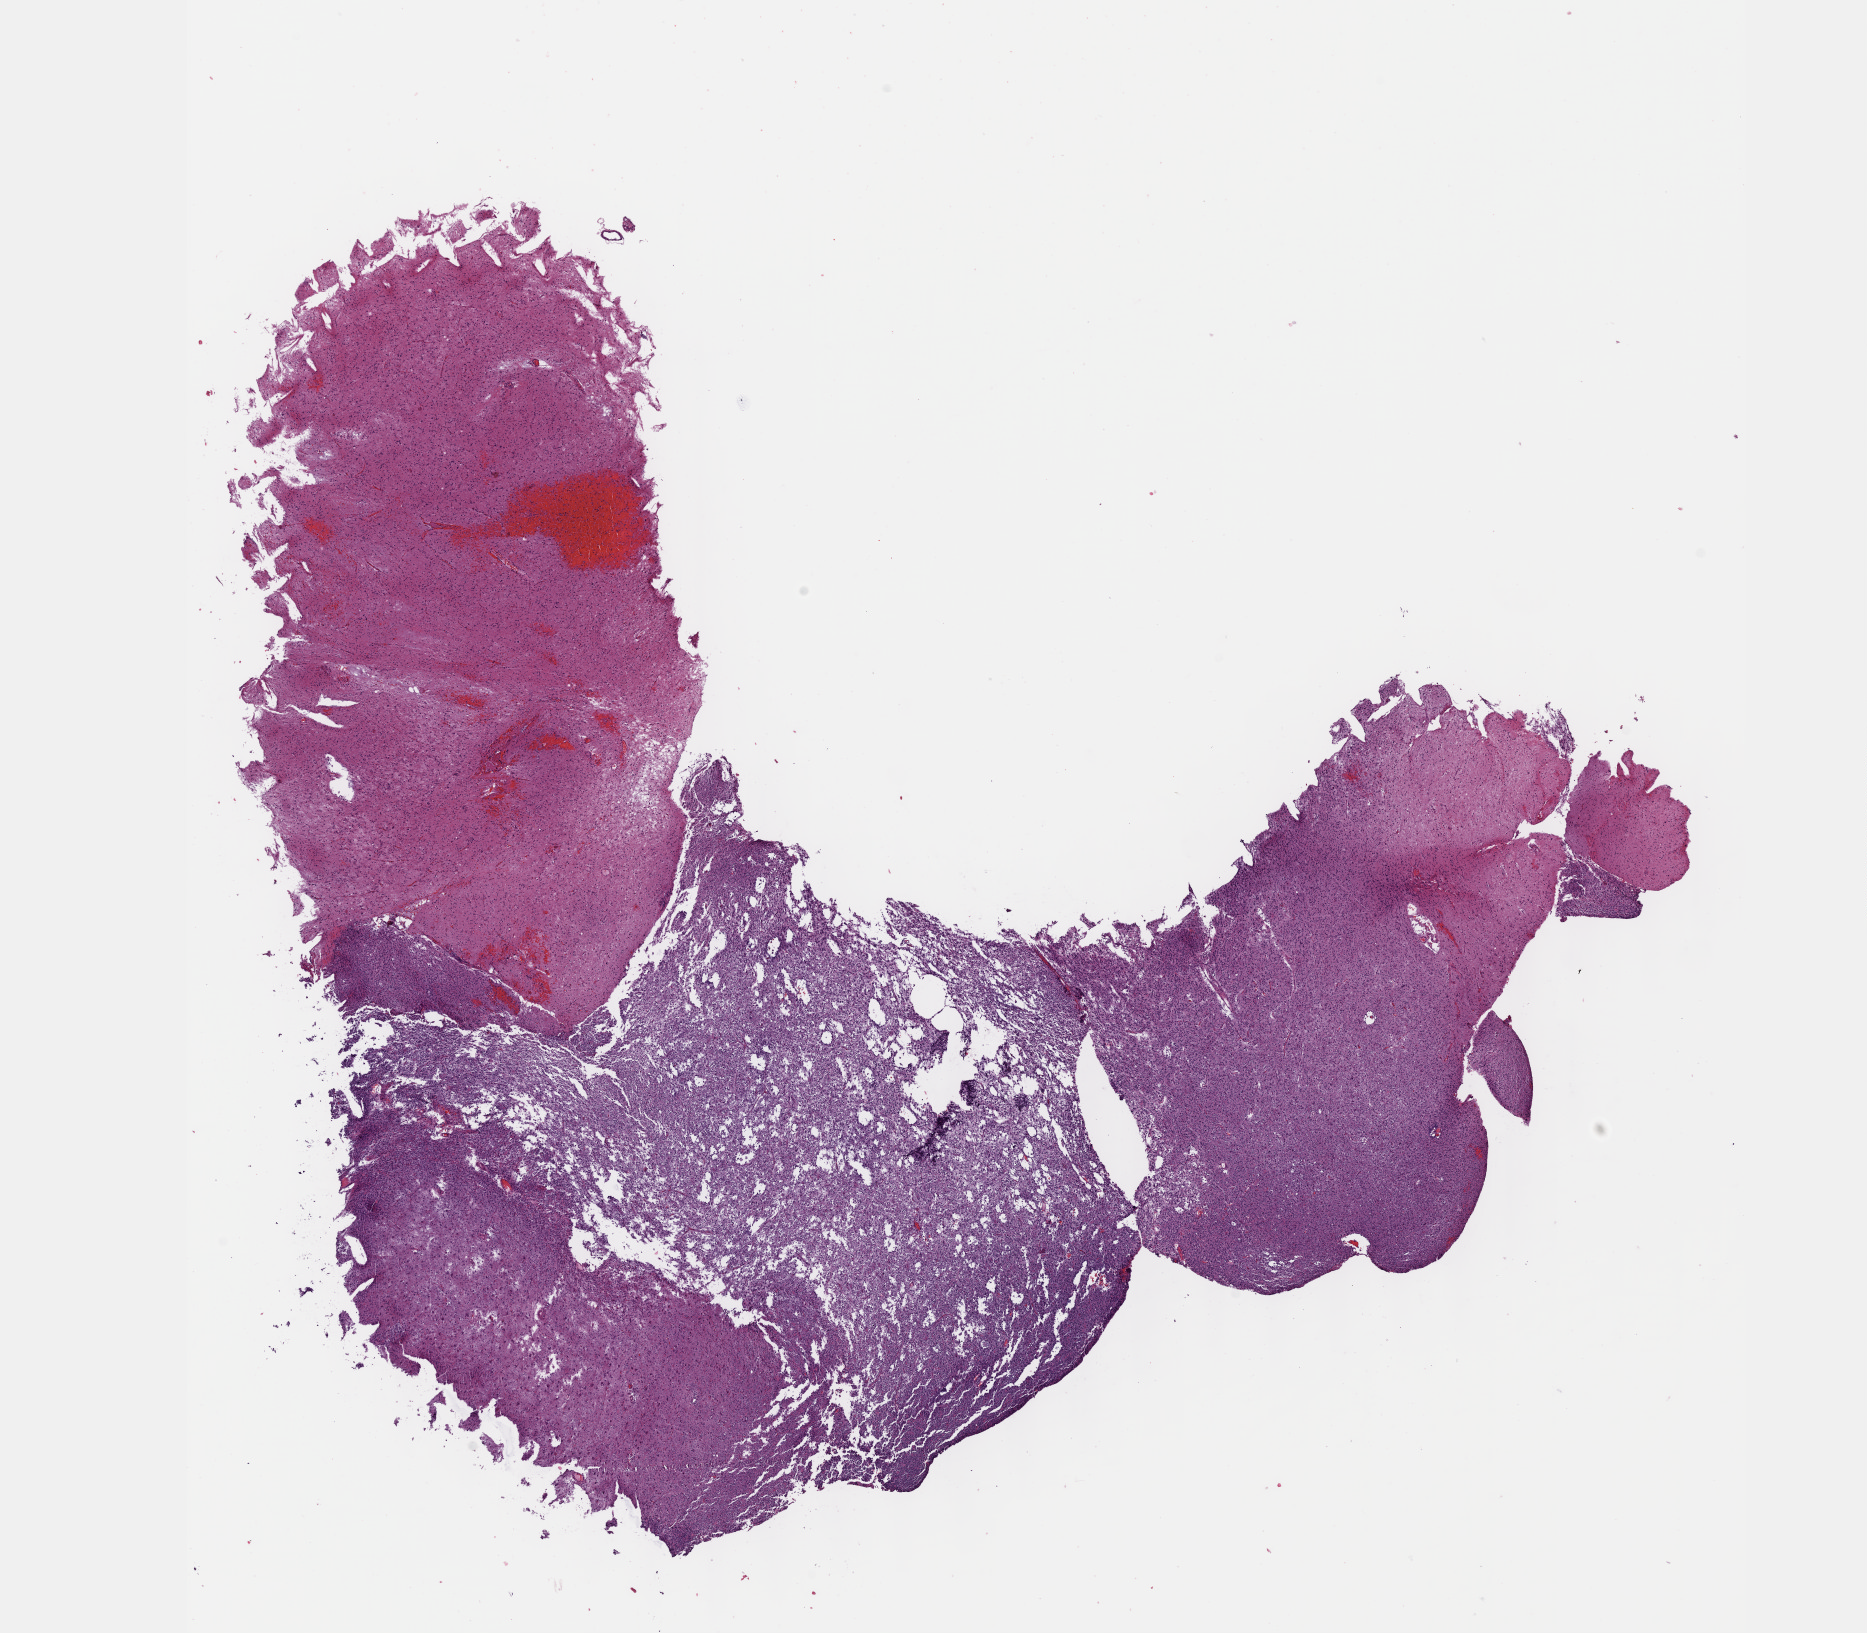
Digitized H&E-stained tissue section (whole slide) — a low-resolution overview of the entire scanned area, about 15.1 x 13.2 mm. FFPE section. Primary tumour sample from the brain. Male patient; age at initial diagnosis 60 years. Histologic grade: G3 (poorly differentiated).
Diagnosis: Oligodendroglioma, anaplastic (cerebrum).